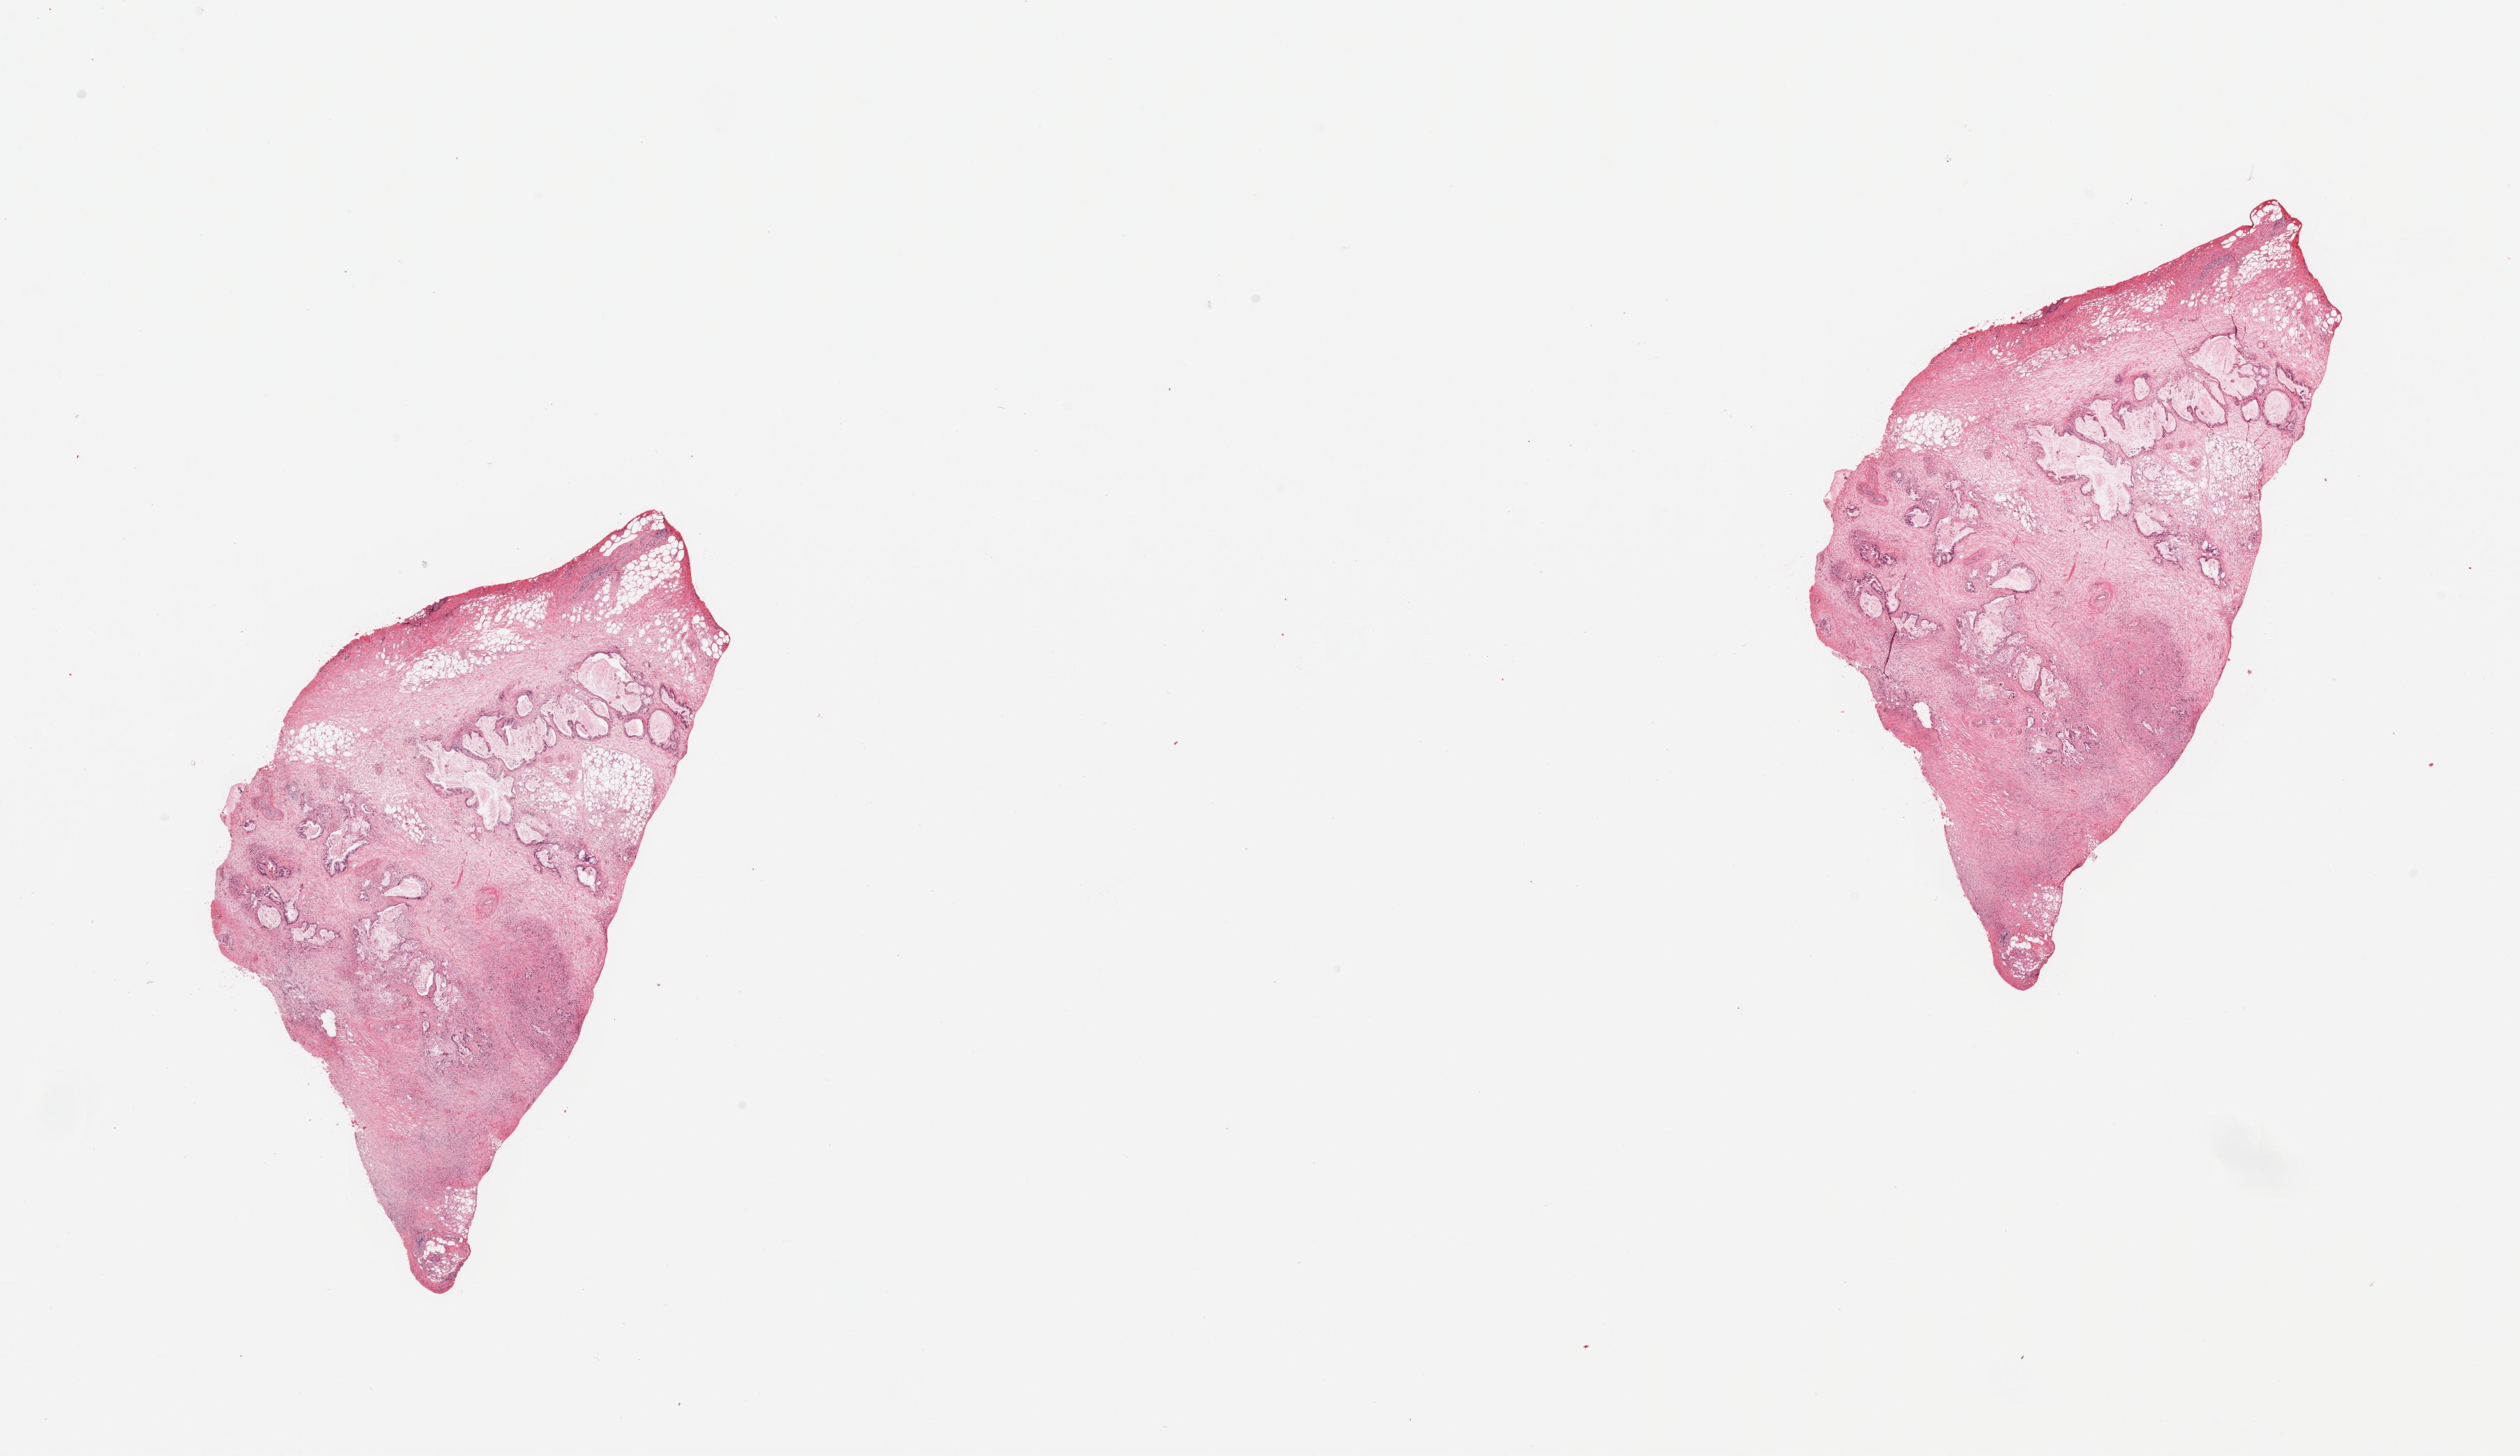
Whole-slide histology image, Hematoxylin and eosin (H&E) stained, shown as a low-resolution overview of the whole scanned area (about 28.5 x 16.5 mm, from a 20x scan); tumour tissue sample, pancreas. Patient: male, age 74 years. Histologic grade: G2 (moderately differentiated).
* histologic diagnosis: Infiltrating duct carcinoma, NOS
* primary tumour site (as recorded): tail
* AJCC pathologic stage: IIA